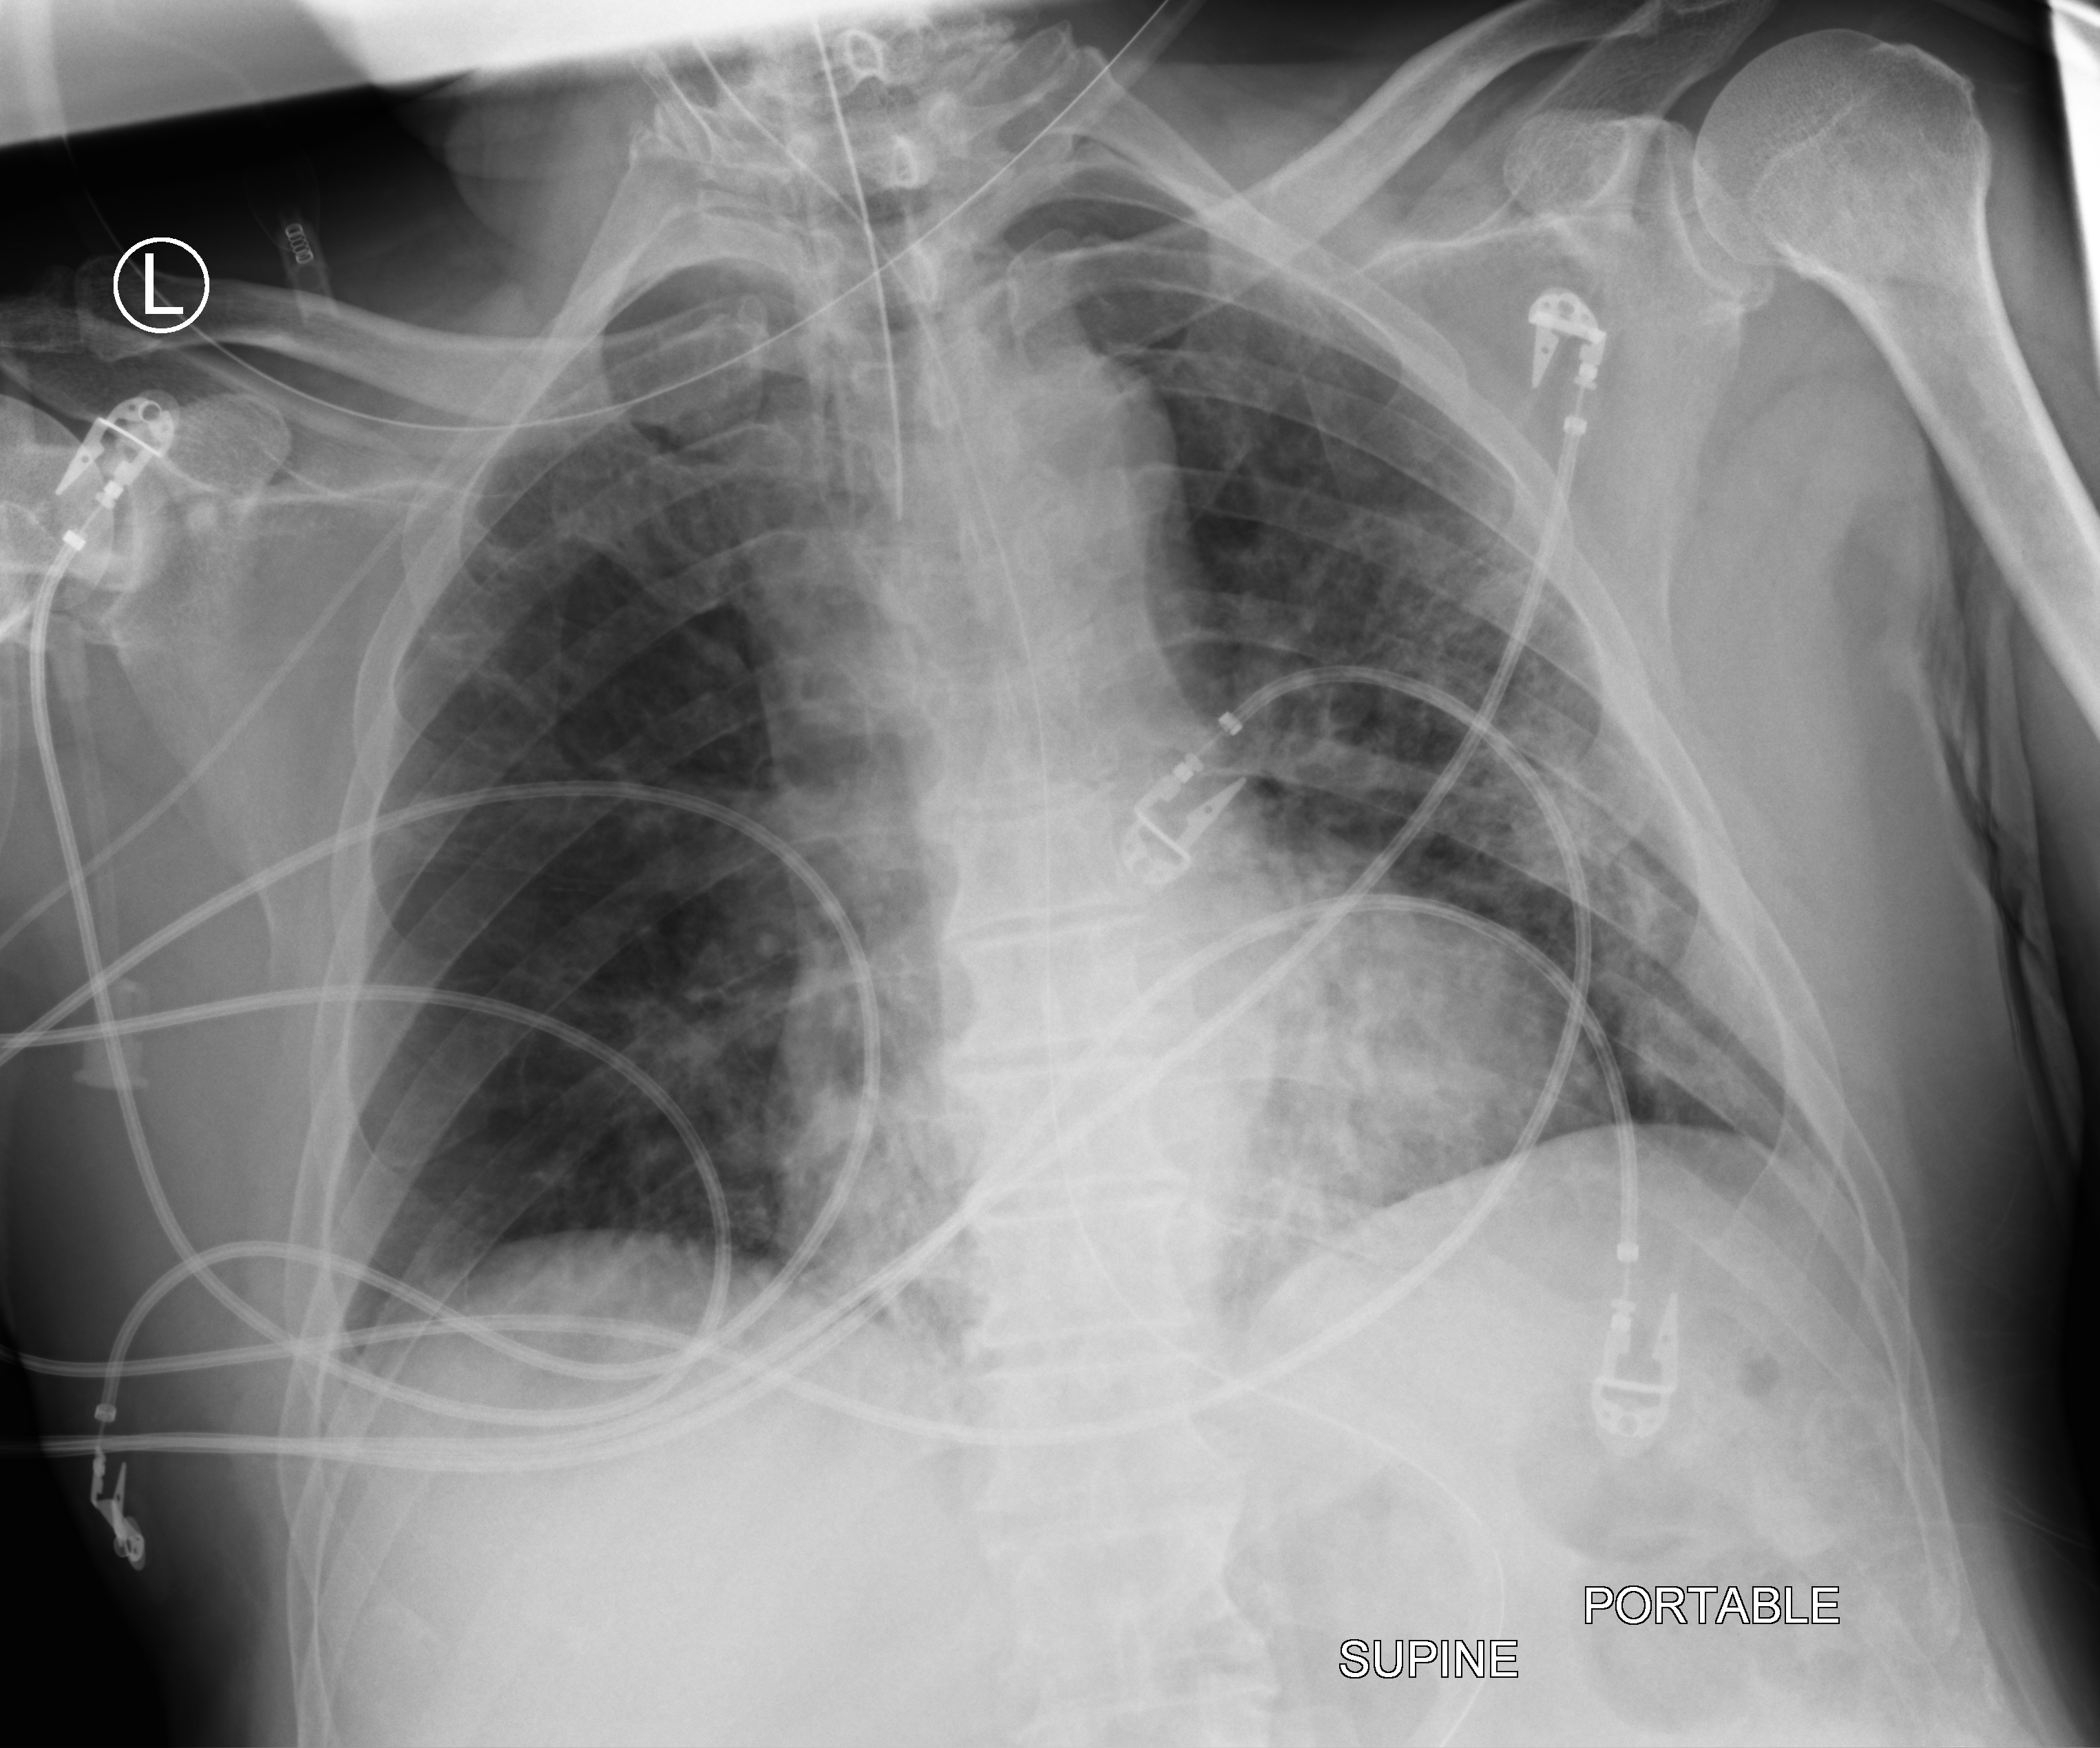
Chest X-ray (portable), anteroposterior (AP) projection. Male patient hospitalised with COVID-19, age 60–74 years.
Admission-level facts for this patient (not findings on this image; timing relative to this image not recorded):
- COPD (admission record): no
- admitted to intensive care during this hospital stay: yes